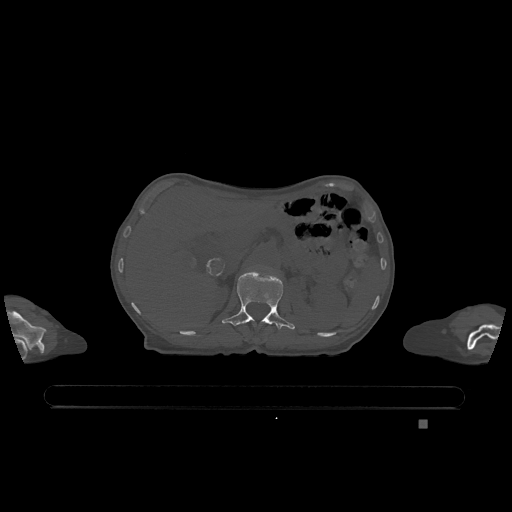
CT including the spine, one axial slice; slice 476 of 1317 in the series (ordered by position); bone window (W 1800 / L 400 HU); 512 × 512 image matrix, field of view 500 × 500 mm. Patient: female, 74 years. Case-level facts recorded for this patient, not image findings: primary cancer: lung.
Outlined on this slice (semi-automatic segmentation, software-assisted and operator-edited):
- L1 vertebra: bounding box <222,271,295,329> (left, top, right, bottom; pixels)